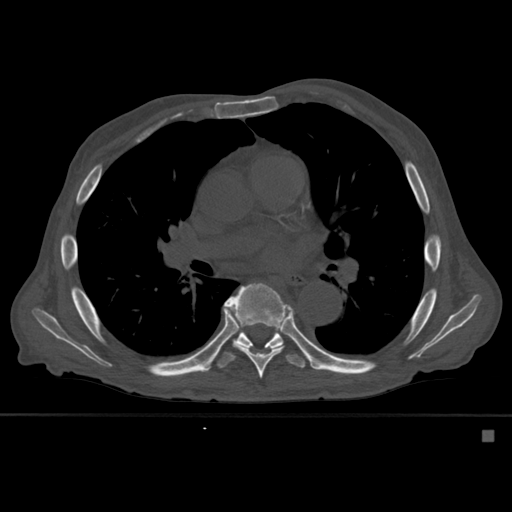
CT including the spine, one axial slice. Slice 361 of 527 in the series (ordered by position). Bone window (W 1800 / L 400 HU). 1.5 mm slice thickness. 512 × 512 image matrix, field of view 373 × 373 mm. Patient: male, 78 years. From the clinical record (not read from this slice): primary cancer: prostate.
Annotated regions visible in this slice (semi-automatically segmented with operator editing):
- T7 vertebra: bounding box [x1, y1, x2, y2] px = [223, 283, 295, 379]
- T8 vertebra: [217, 330, 306, 369]